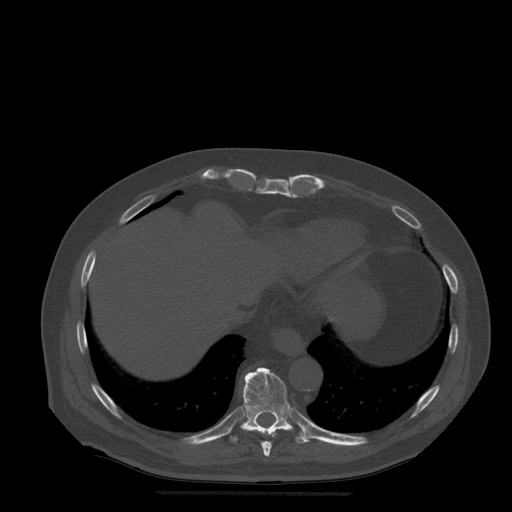
CT including the spine, one axial slice. Position 275 of 522 along the scan axis. Bone window (W 1800 / L 400 HU). 512 × 512 image matrix. Patient age 72 years. From the clinical record (not read from this slice): primary cancer: prostate.
Outlined on this slice (semi-automatically segmented with operator editing):
- T10 vertebra: bounding box (x1, y1, x2, y2) in pixels: (232, 368, 313, 444)
- T9 vertebra: (261, 441, 272, 457)